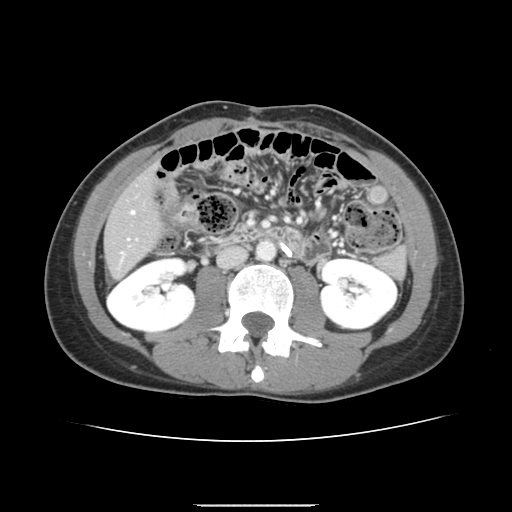
Contrast-enhanced abdominal CT, one axial slice; position 49 of 150 along the scan axis; 120 kVp; intravenous contrast given; soft-tissue window (W 400 / L 40 HU); 512 × 512 image matrix. Female patient, age 32 years. From the clinical record (not read from this slice): diagnosis: colorectal cancer liver metastases, imaged before liver resection; multiple liver metastases: yes; largest metastasis: 0.7 cm; disease in both lobes: no.
Annotated regions visible in this slice (outlined manually by an expert reader):
- hepatic veins: bounding box <131,211,134,213> (left, top, right, bottom; pixels)
- liver: <106,170,160,277>
- planned liver remnant (the part of the liver to remain after resection): <105,171,160,277>
- portal vein (with intrahepatic branches): <121,252,124,255>